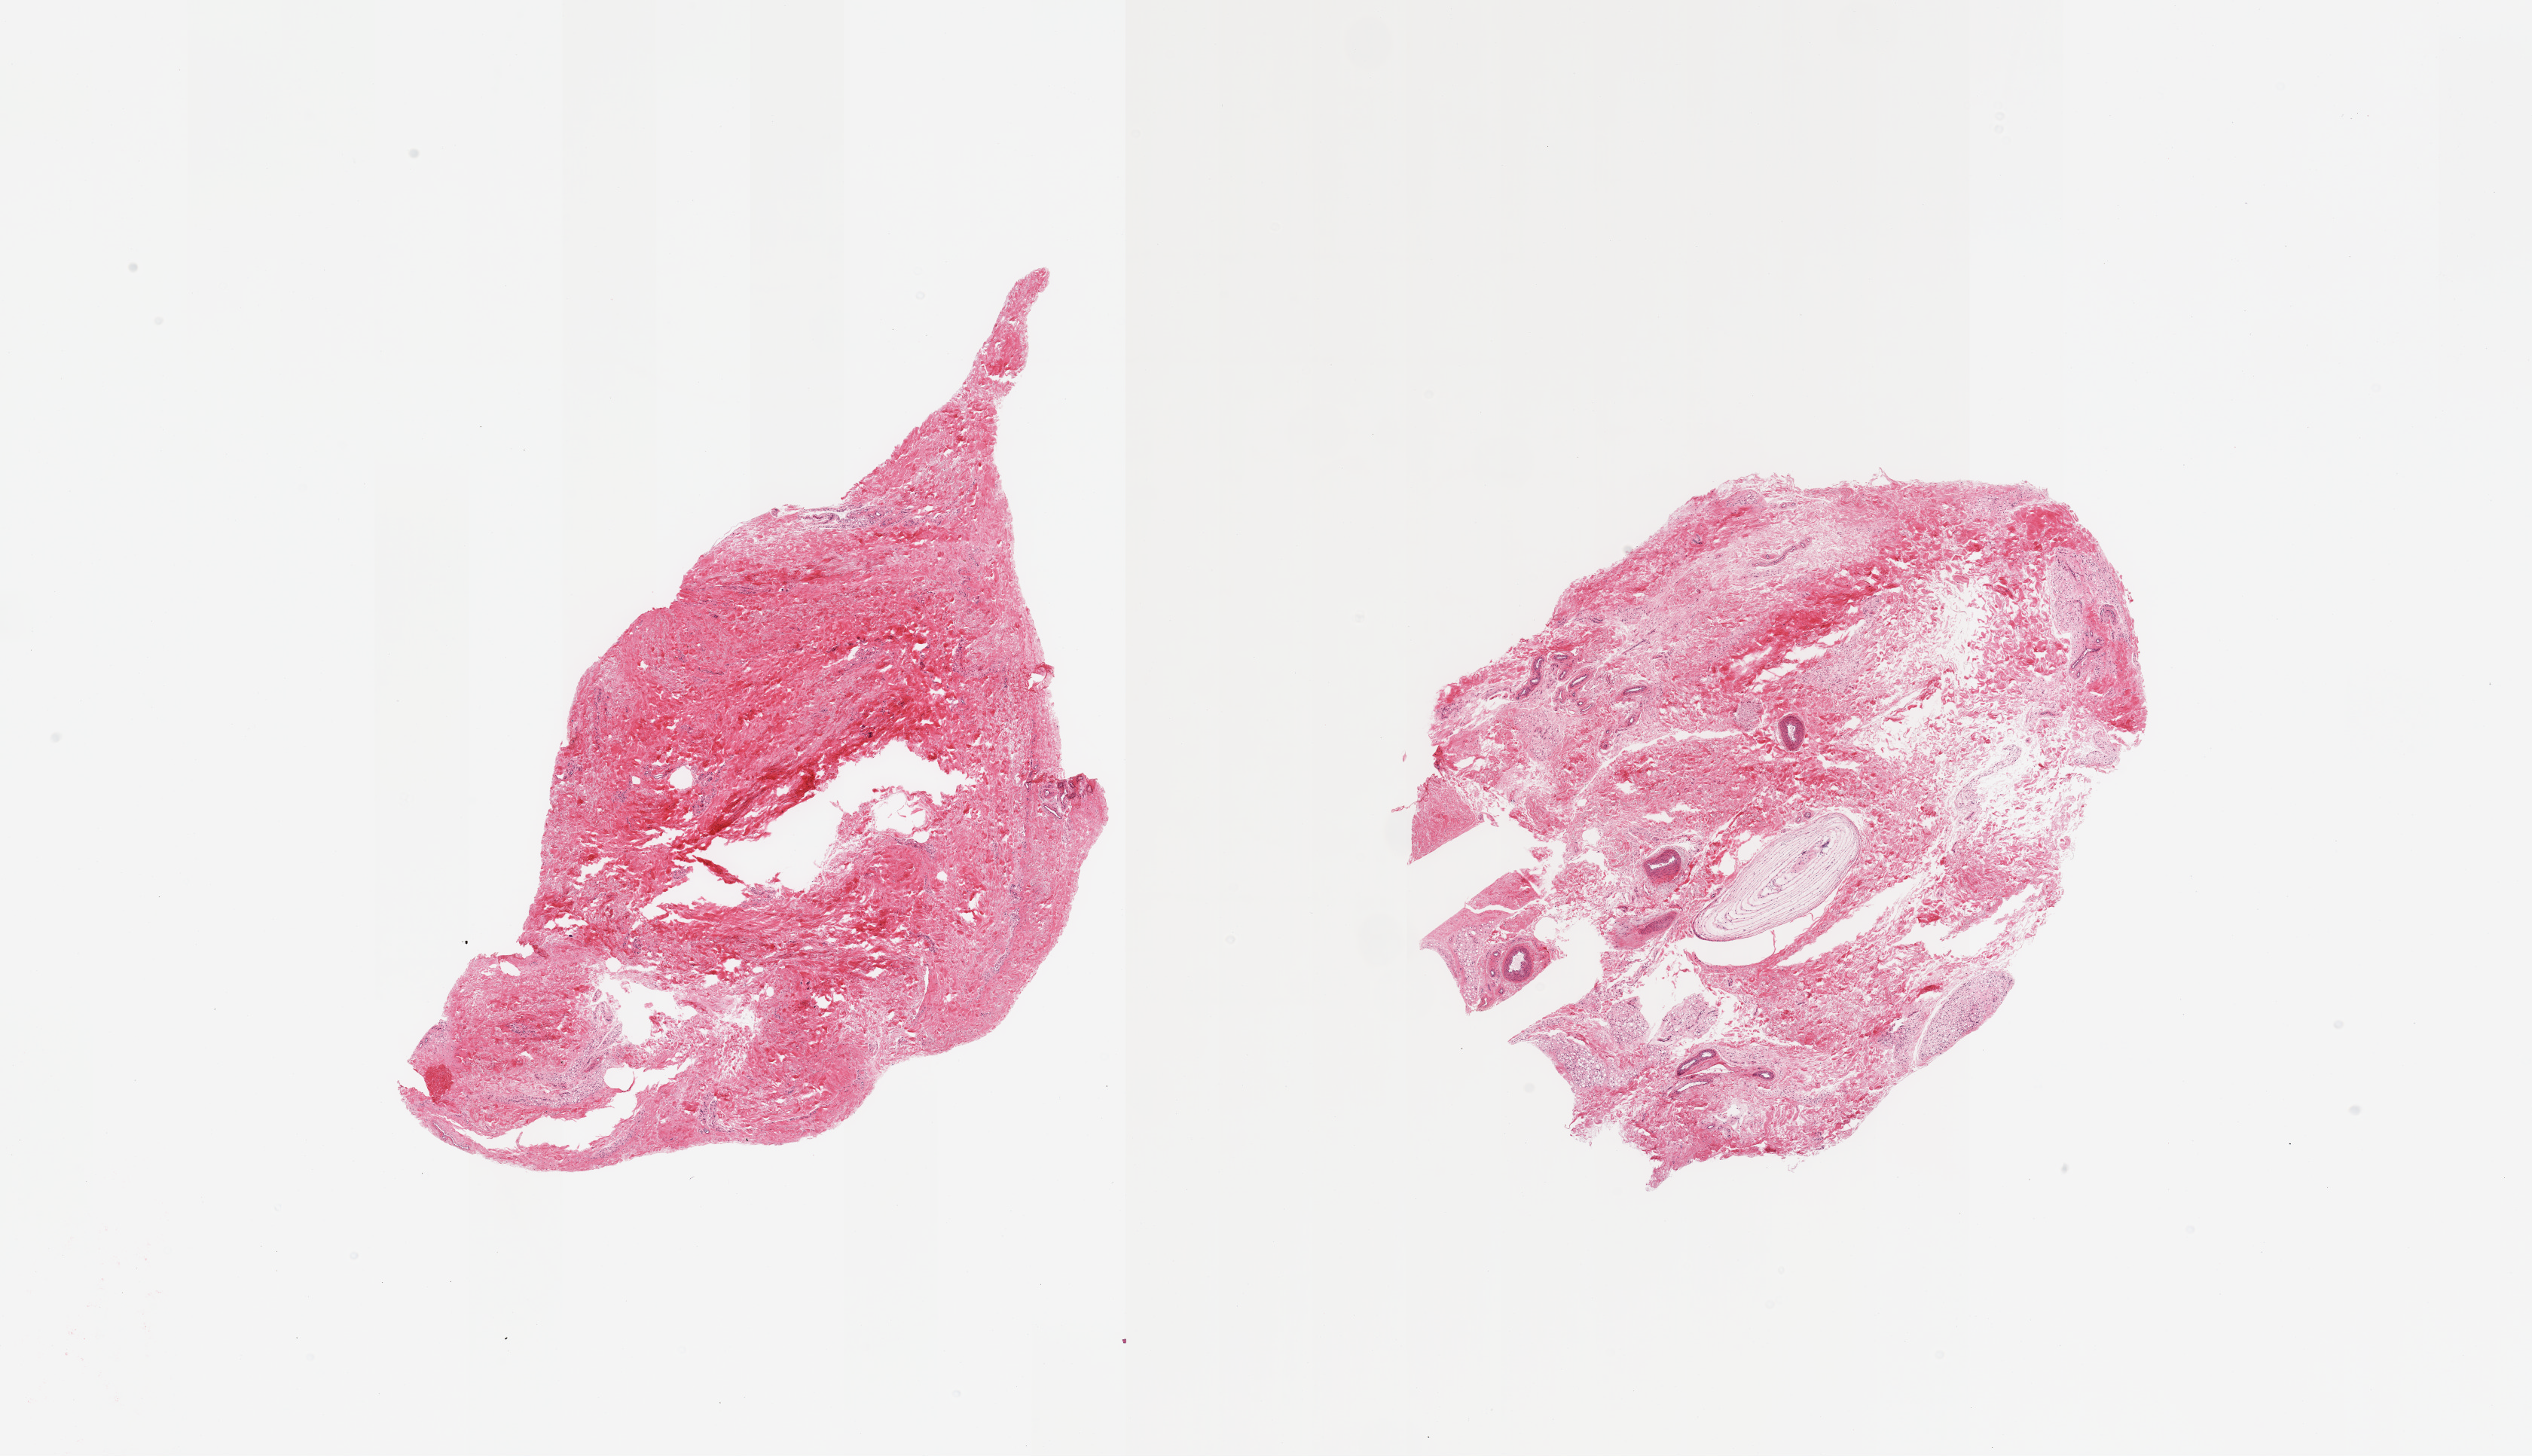
Haematoxylin and eosin whole-slide image, brightfield — low-resolution overview of the scanned area, about 26.6 x 15.3 mm (acquisition: 20x scan). PAXgene-fixed paraffin-embedded (PFPE) section. Sampled site (target tissue): breast. Tissue donor sample. Donor: male.
Pathologist's review note for this sample: 2 pieces; predominantly stroma with large pacinian corpuscle, atrophy of fat.